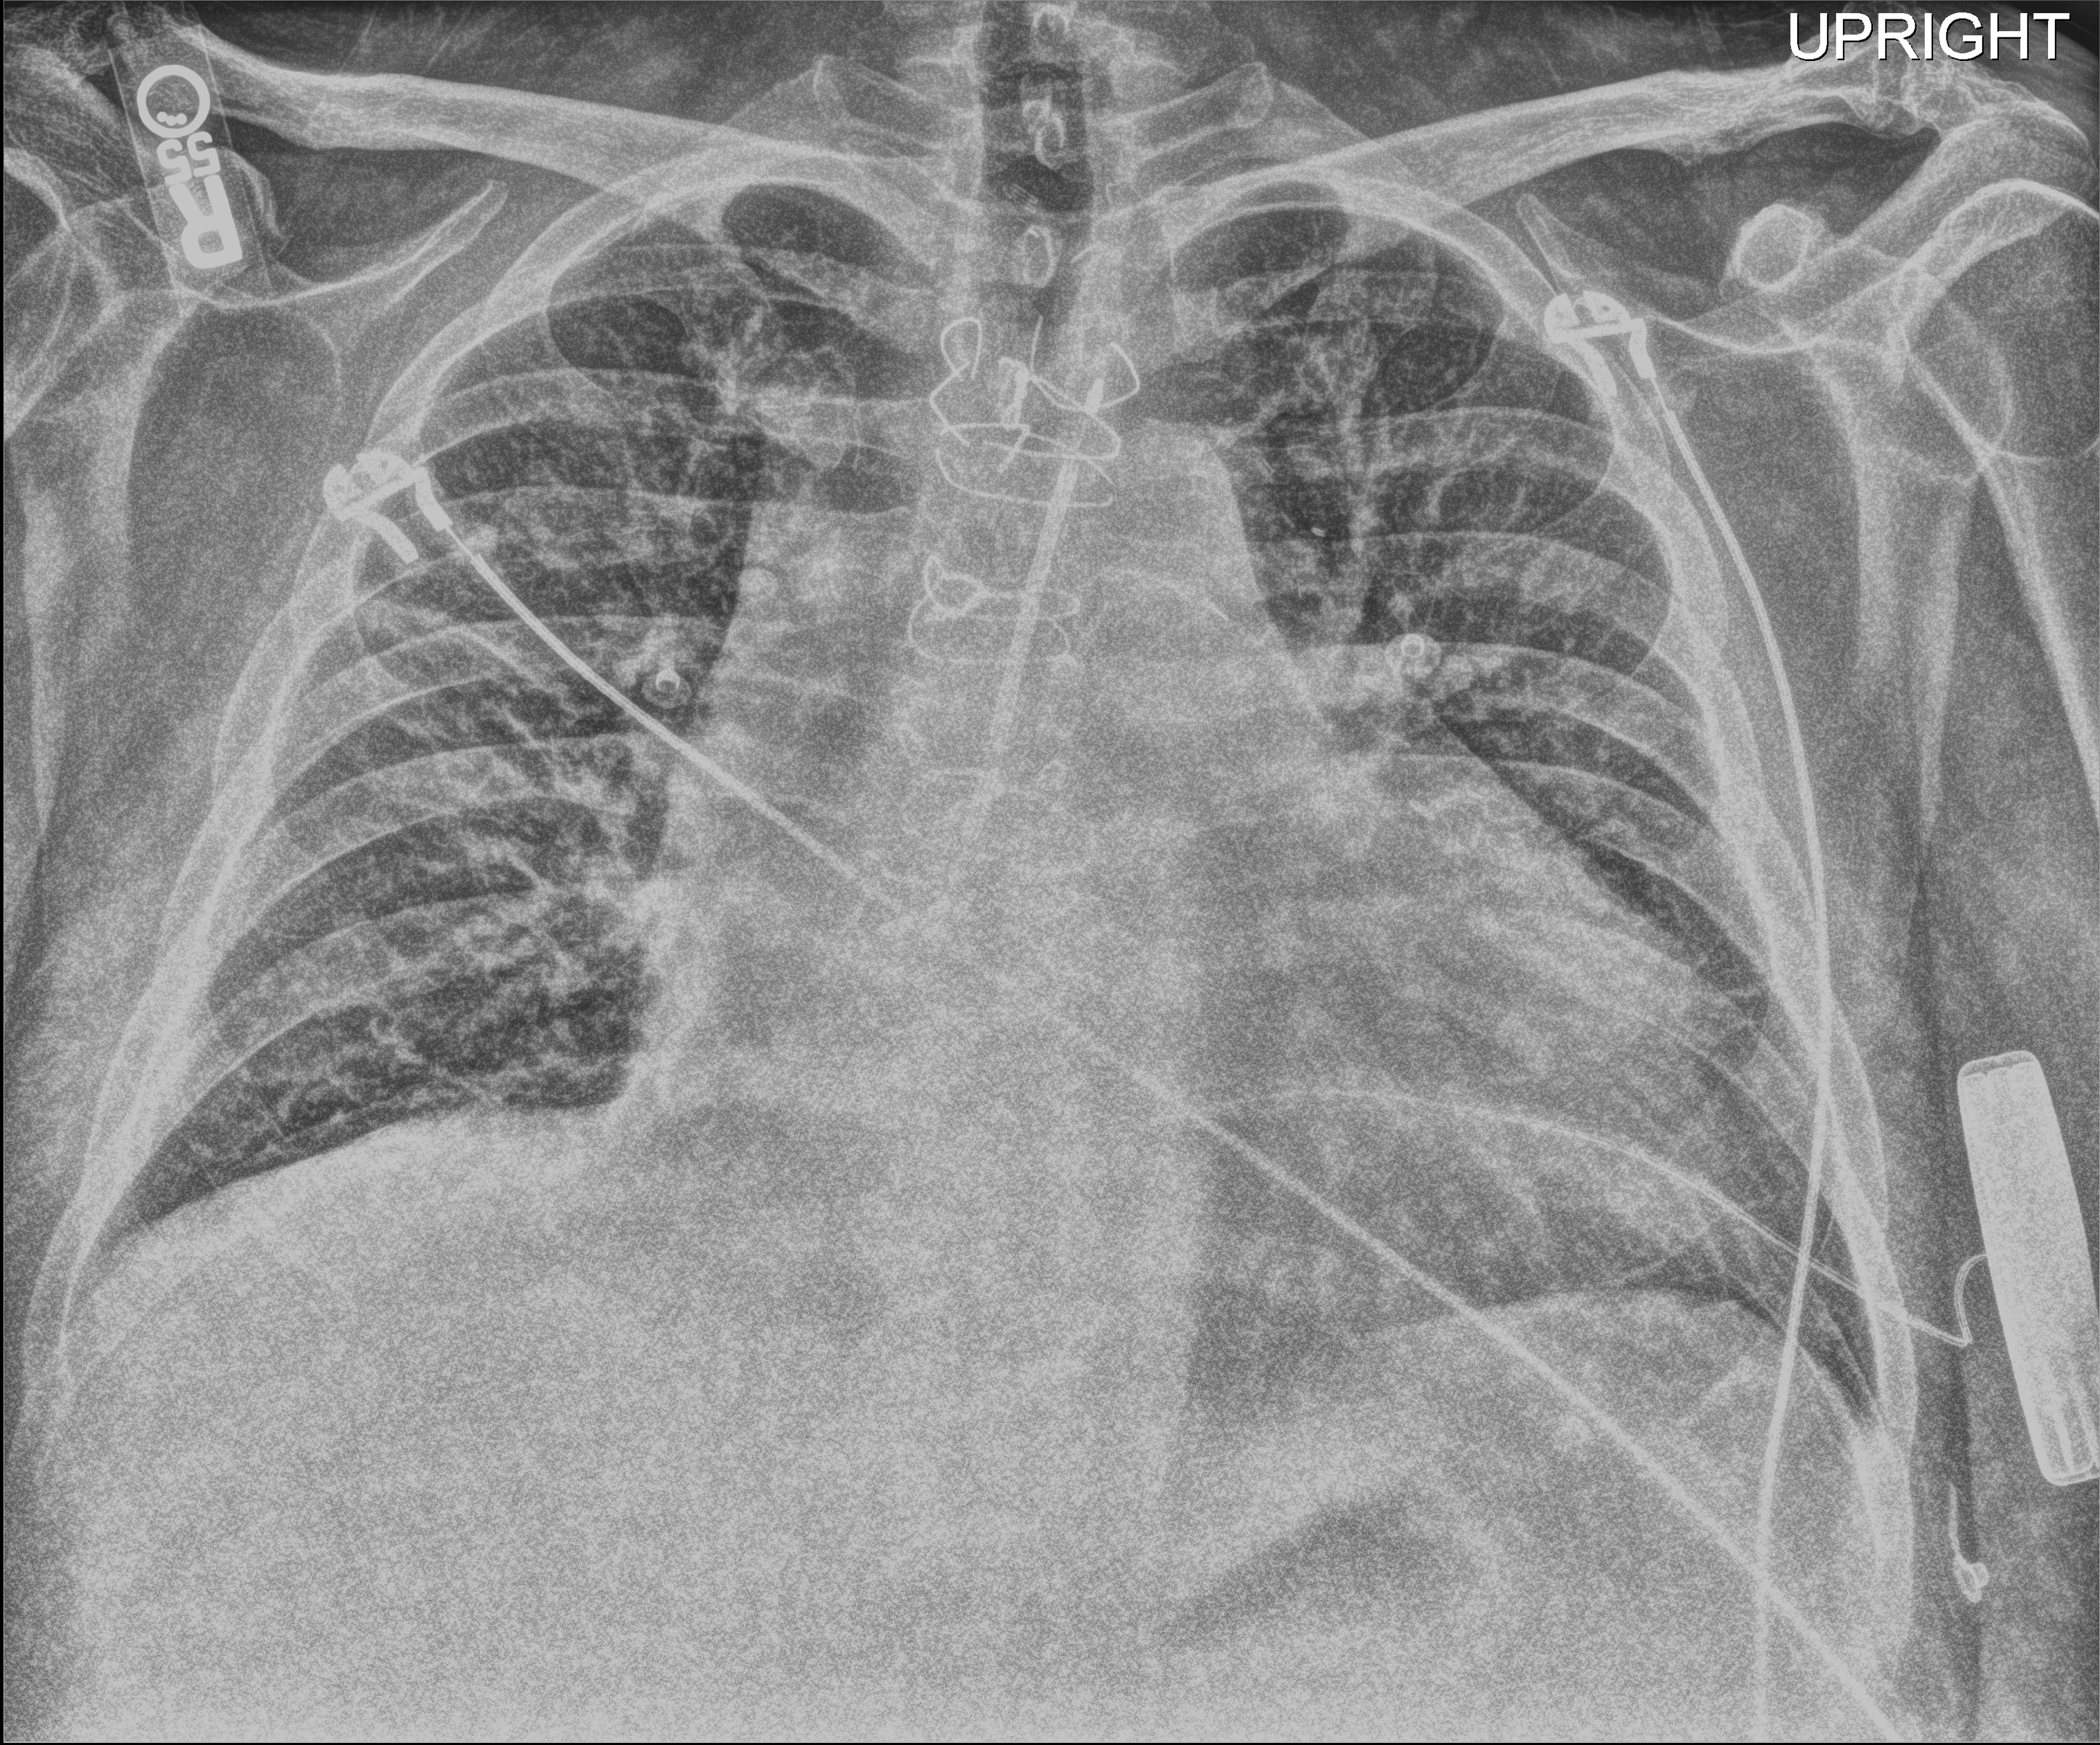
Chest radiograph (digital radiography); anteroposterior (AP) projection. Patient hospitalised with COVID-19; male, aged 60–74 years.
Hospital-stay facts (about this admission, not read from this image; timing relative to this image not recorded):
- mechanically ventilated during this hospital stay: no